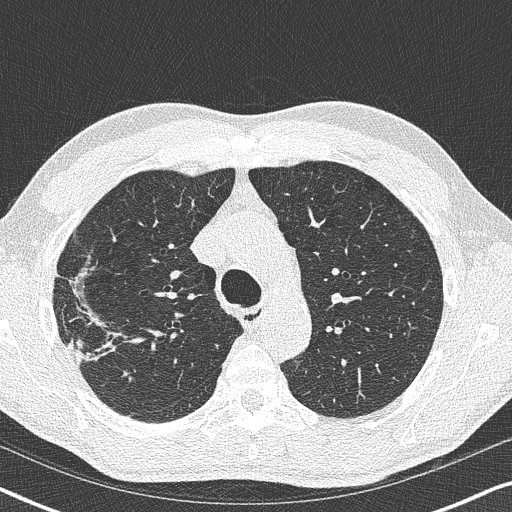
Low-dose screening chest CT, one axial slice; position 267 of 356 along the scan axis; reconstruction kernel B50f; lung window (W 1500 / L -600 HU); 512 × 512 image matrix, field of view 330 × 330 mm.
Structures marked on this image (manually delineated by an expert):
- lesion 1 (tumor, upper lobe of right lung): bounding box [x1, y1, x2, y2] px = [68, 338, 88, 368]